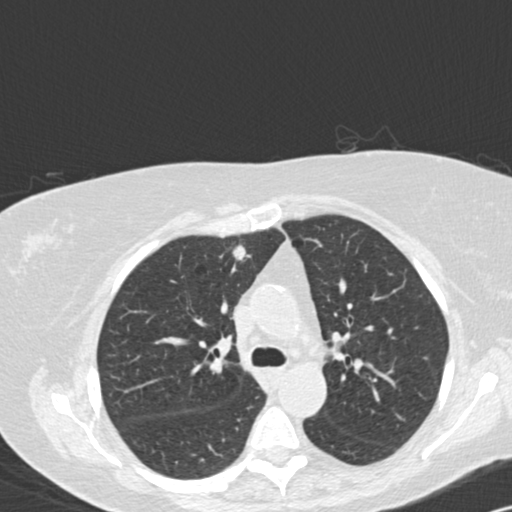
Chest CT (low-dose screening protocol), one axial image. Third annual screen. Lung window (W 1500 / L -600 HU). 2 mm slice thickness. Standard (soft-tissue) reconstruction kernel (B30f). 120 kVp. 512 × 512 image matrix, field of view 328 × 328 mm. Female, age 72 years at enrolment.
• Expert reader's lesion annotation, bounding box [x1, y1, x2, y2] px = [218, 235, 264, 278].
• The exam's reader record, not a measurement of the box and not confirmed to be the same lesion: non-calcified nodule or mass ≥4 mm, right upper lobe, 8 × 8 mm, spiculated (stellate) margins, soft tissue attenuation, pre-existing on the prior screen: yes; interval growth: yes.
• Official screen result: positive, other.
• Lung cancer was diagnosed 154 days after this screen: adenocarcinoma, NOS, right upper lobe, moderately differentiated (G2), stage IA (AJCC 6th edition), 15 mm at pathology.